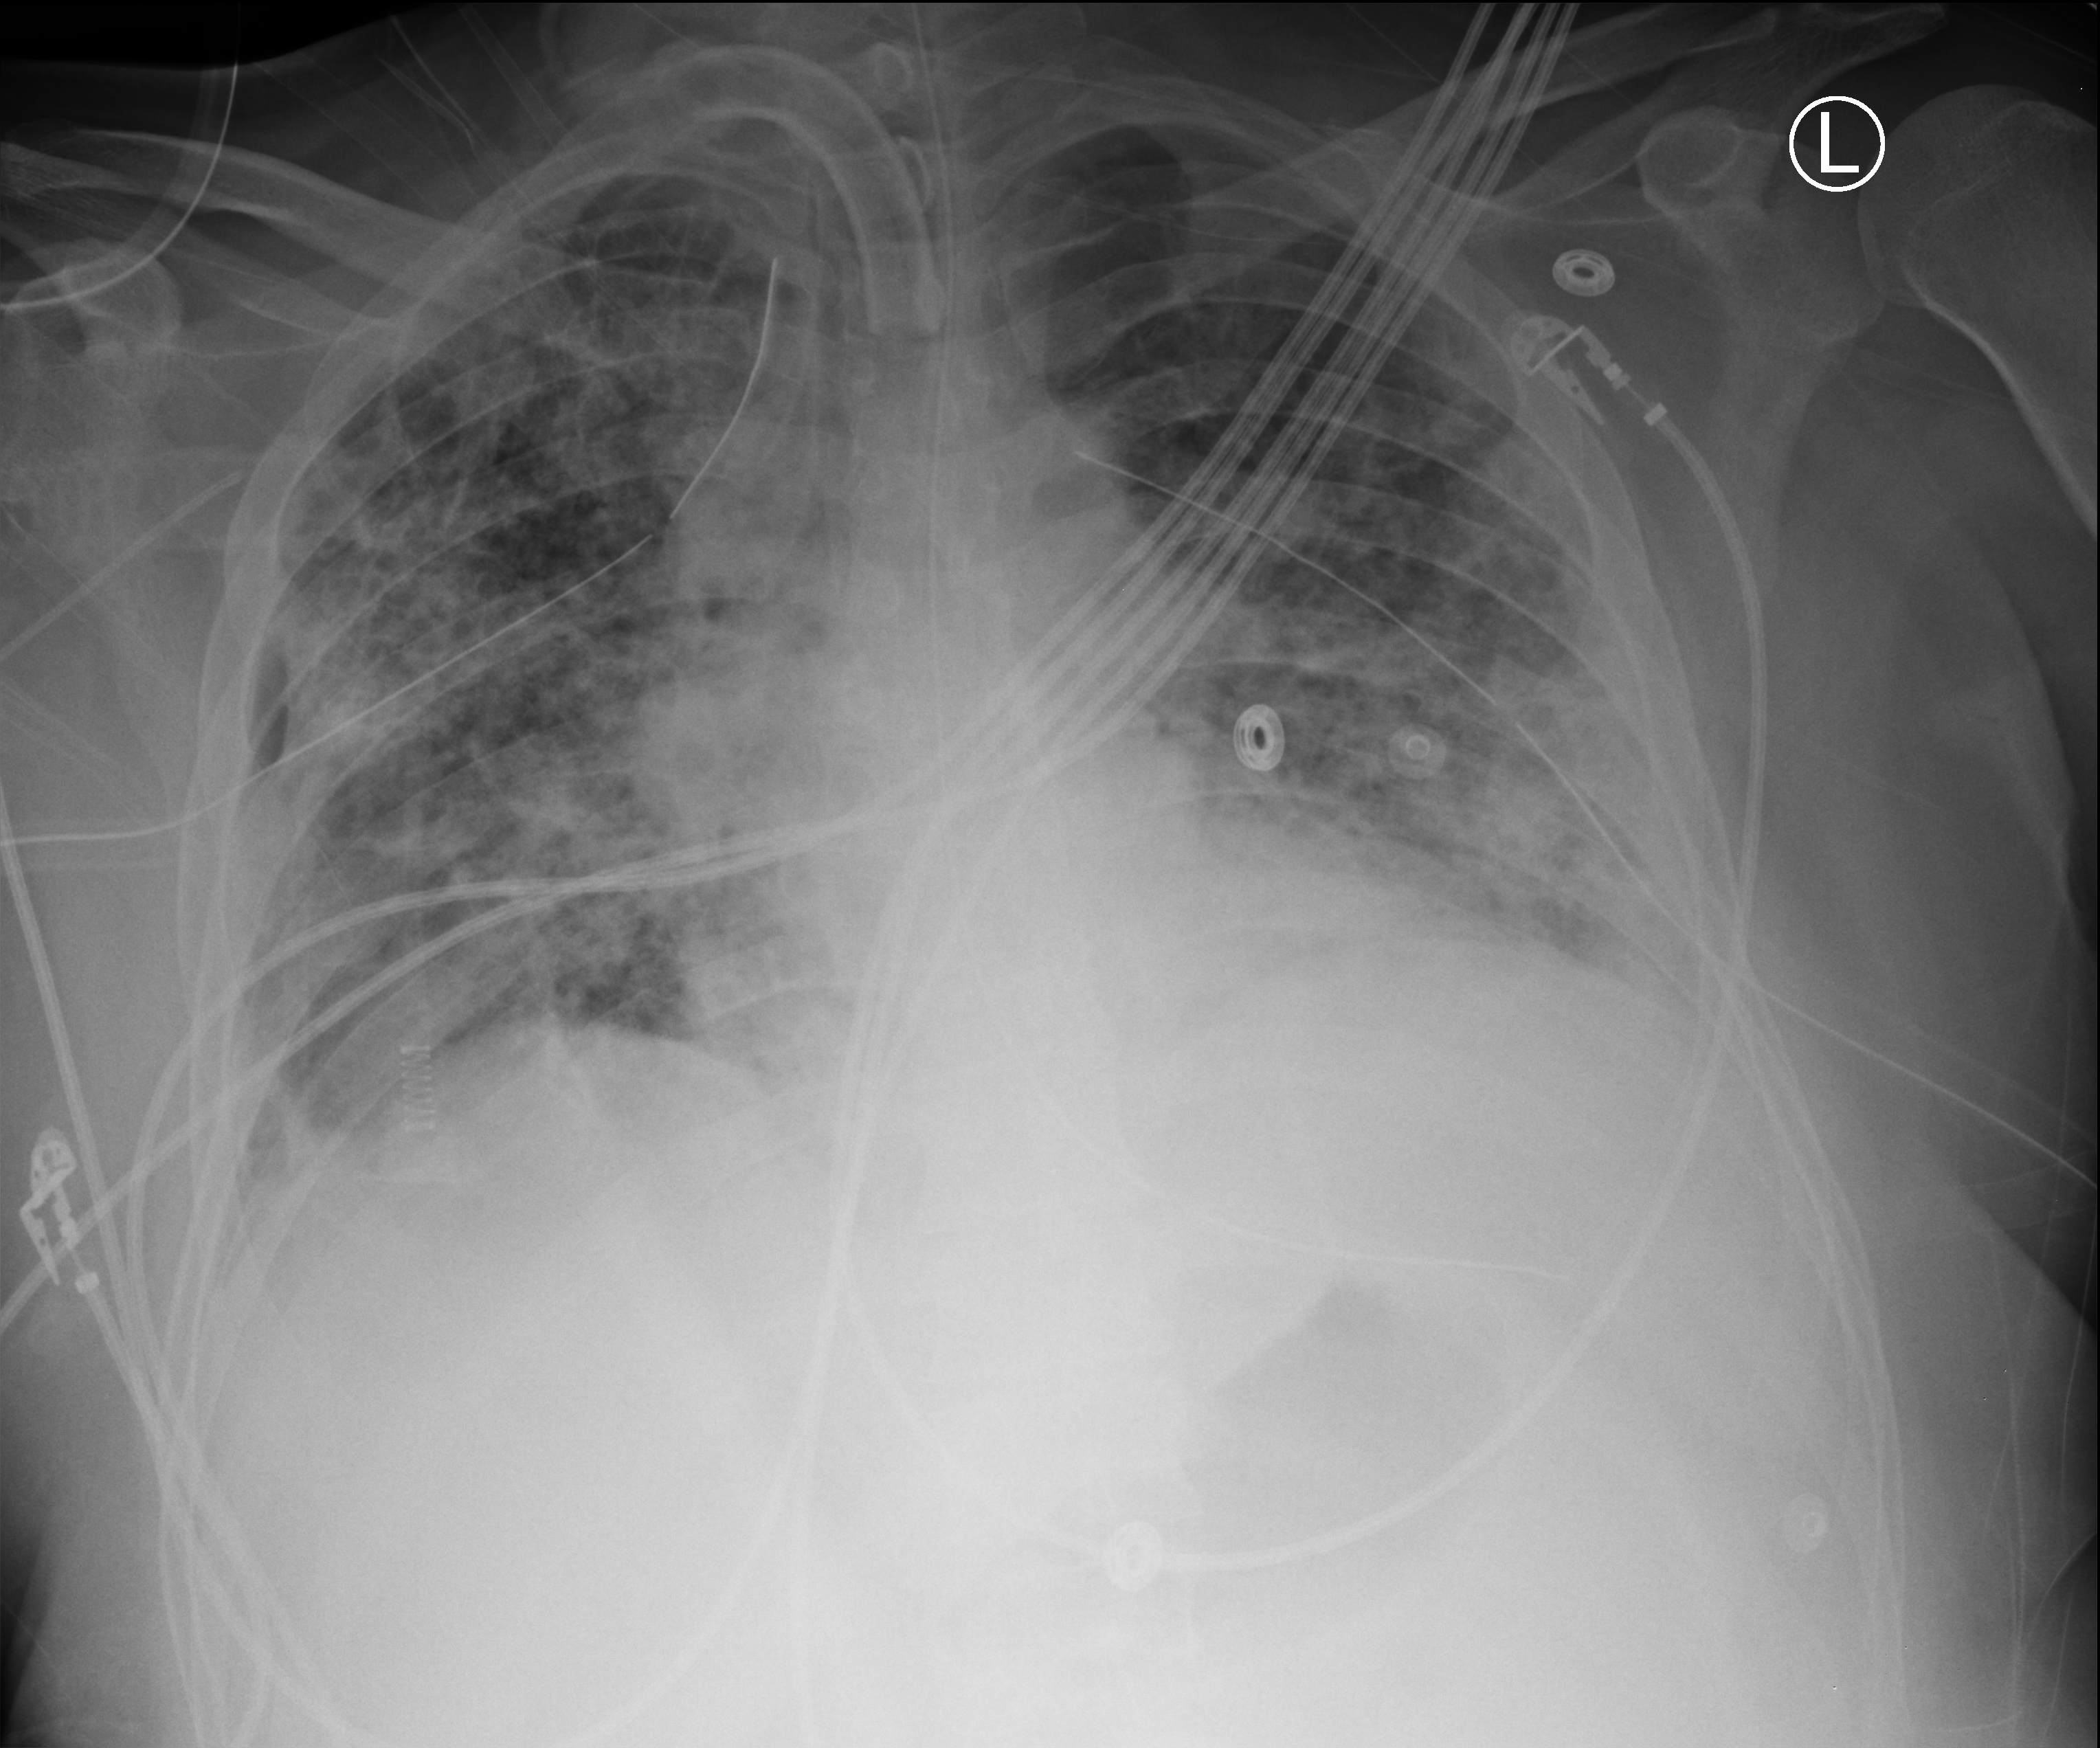
Portable chest radiograph, anteroposterior (AP) projection. Patient hospitalised with COVID-19; male, aged 18–59 years.
Admission-level facts for this patient (not findings on this image; timing relative to this image not recorded):
- mechanically ventilated during this hospital stay: yes